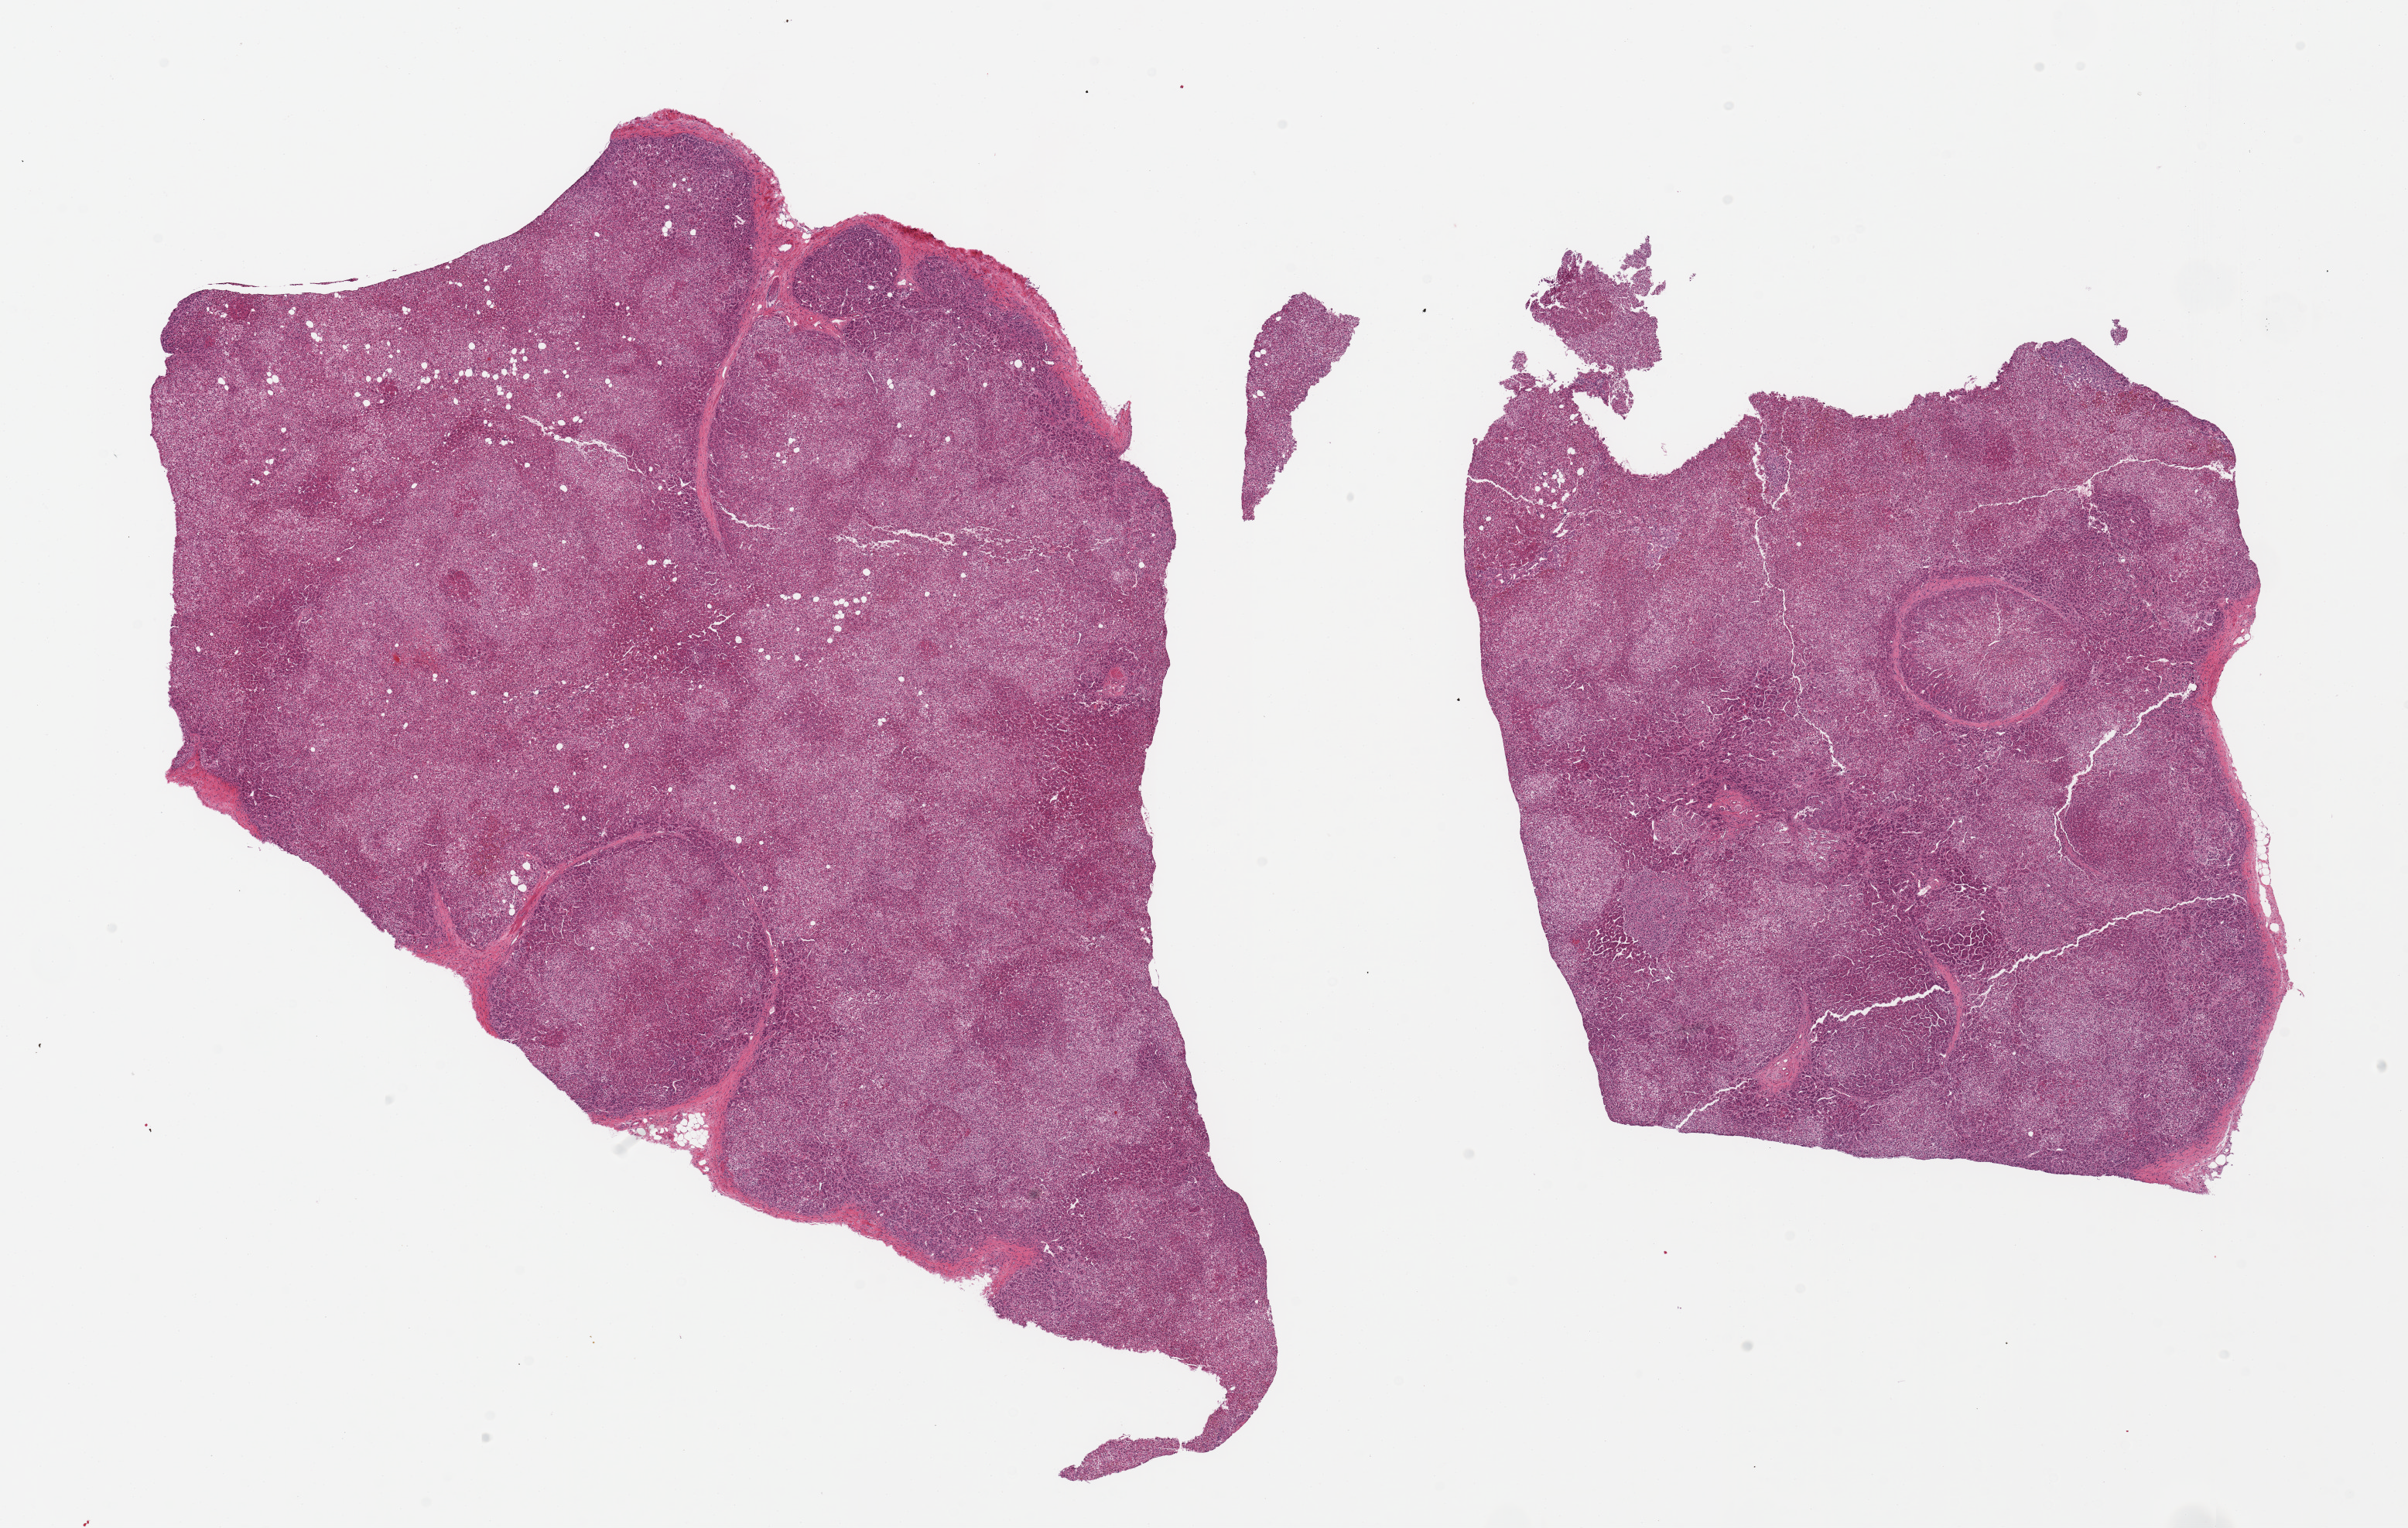
Hematoxylin and eosin (H&E) whole-slide image, brightfield, a low-resolution overview of the entire scanned area, about 24.6 x 15.6 mm, PAXgene-fixed, paraffin-embedded tissue, sampled site (target tissue): adrenal gland, donor tissue sample. Donor sex: male.
Pathologist's review note for this sample: 2 pieces, cortex.